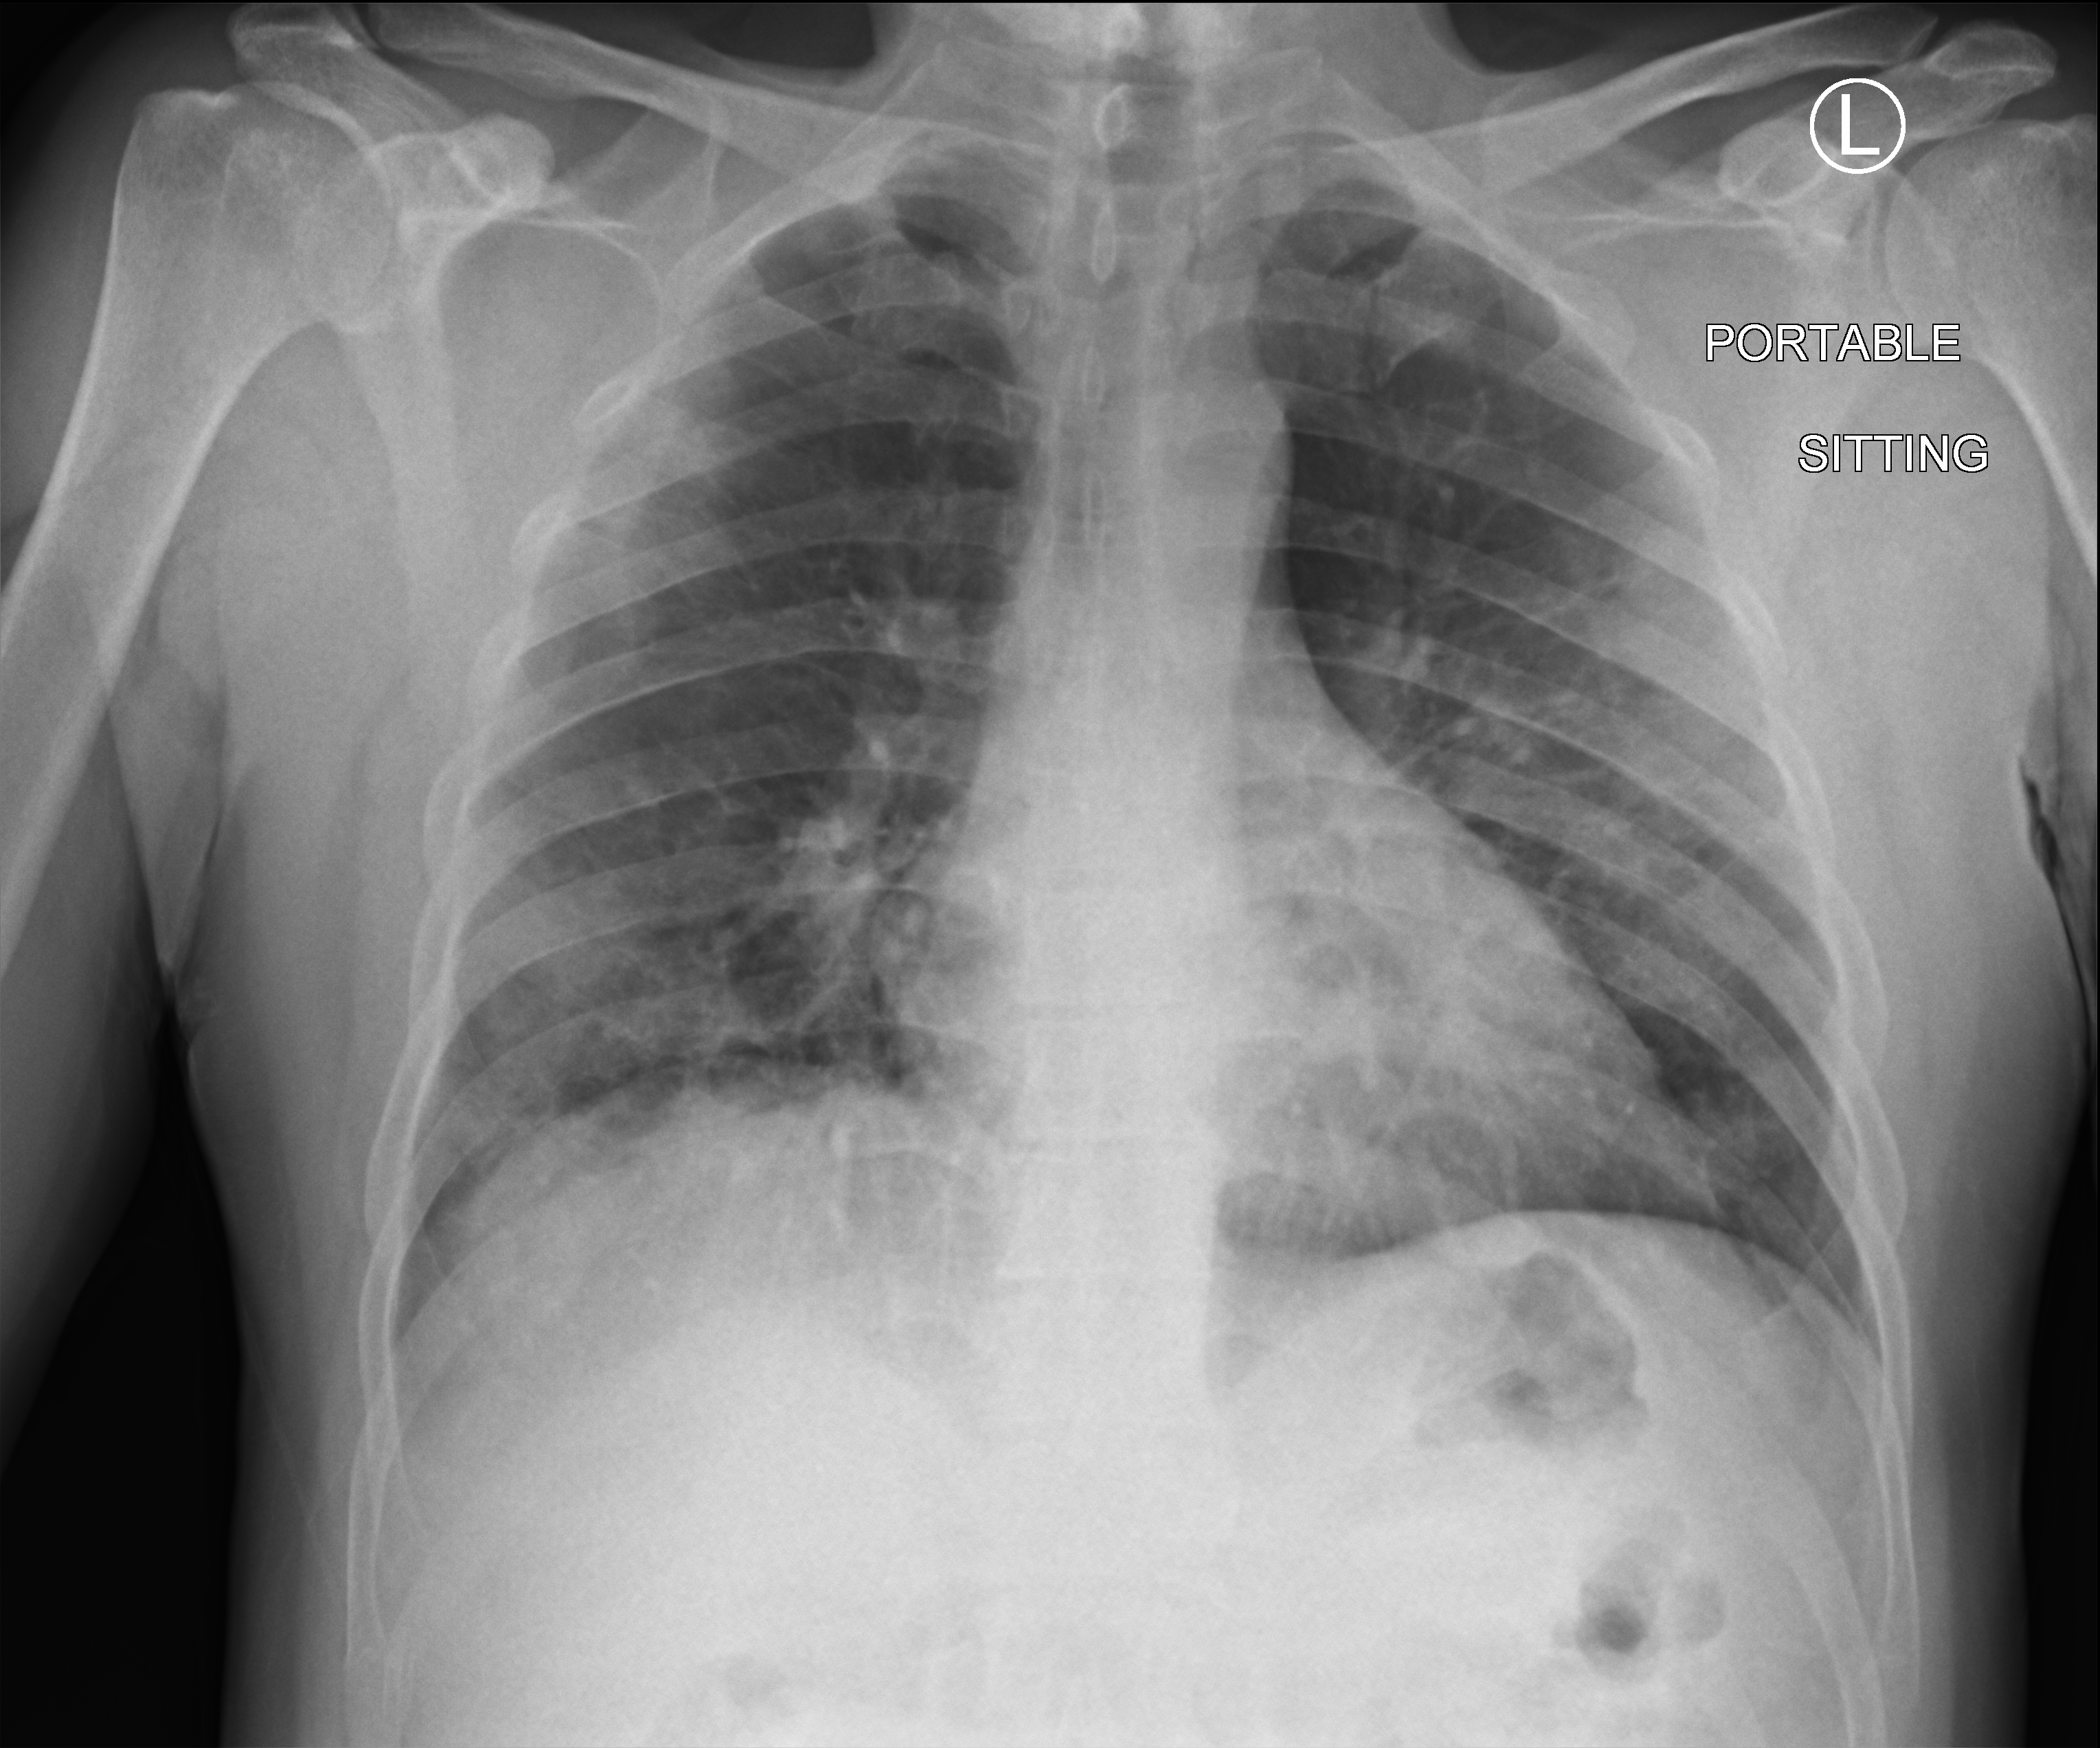
Bedside chest radiograph (computed radiography); anteroposterior (AP) projection. Patient hospitalised with COVID-19; male, aged 18–59 years.
Hospital-stay facts (about this admission, not read from this image; timing relative to this image not recorded): mechanically ventilated during this hospital stay: no.